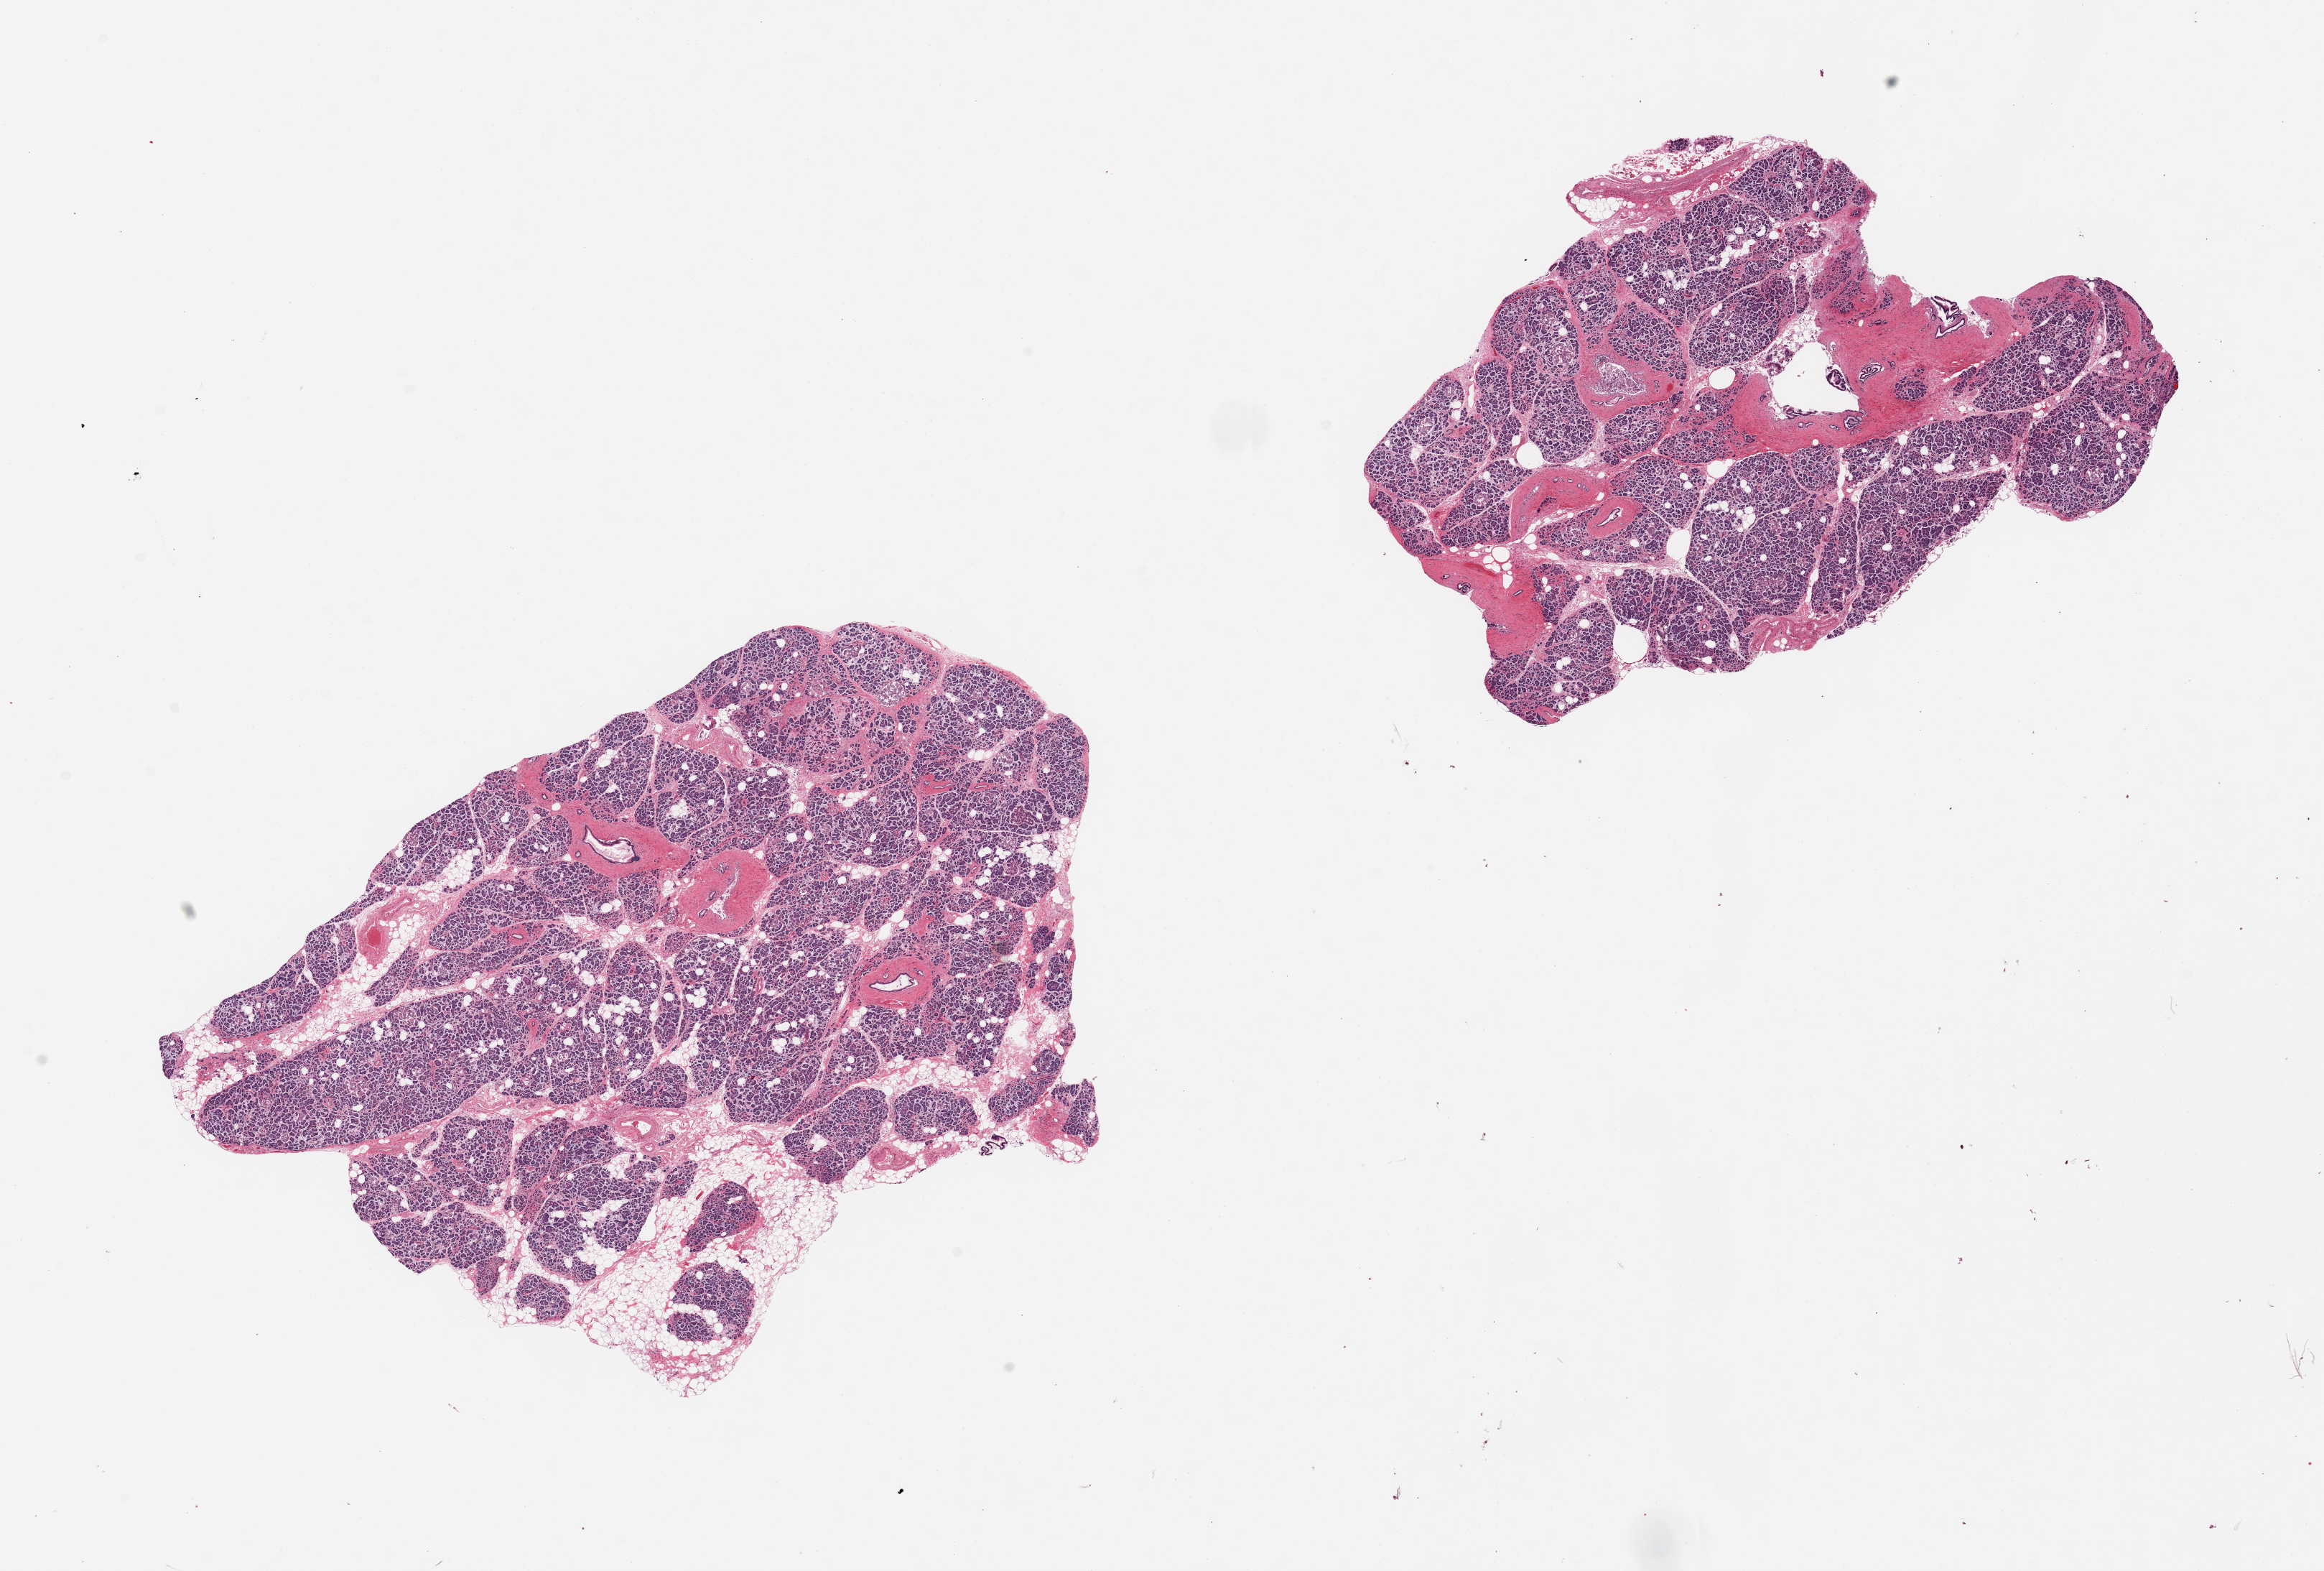
Hematoxylin and eosin (H&E) whole-slide image, shown as a low-resolution overview of the whole scanned area (about 25.6 x 17.3 mm, from a 20x scan). PAXgene-fixed, paraffin-embedded tissue. Sampled site (target tissue): pancreas. Donor tissue sample. Female donor.
* reviewer comment on this tissue sample: 2 pieces, marked saponification/autolysis